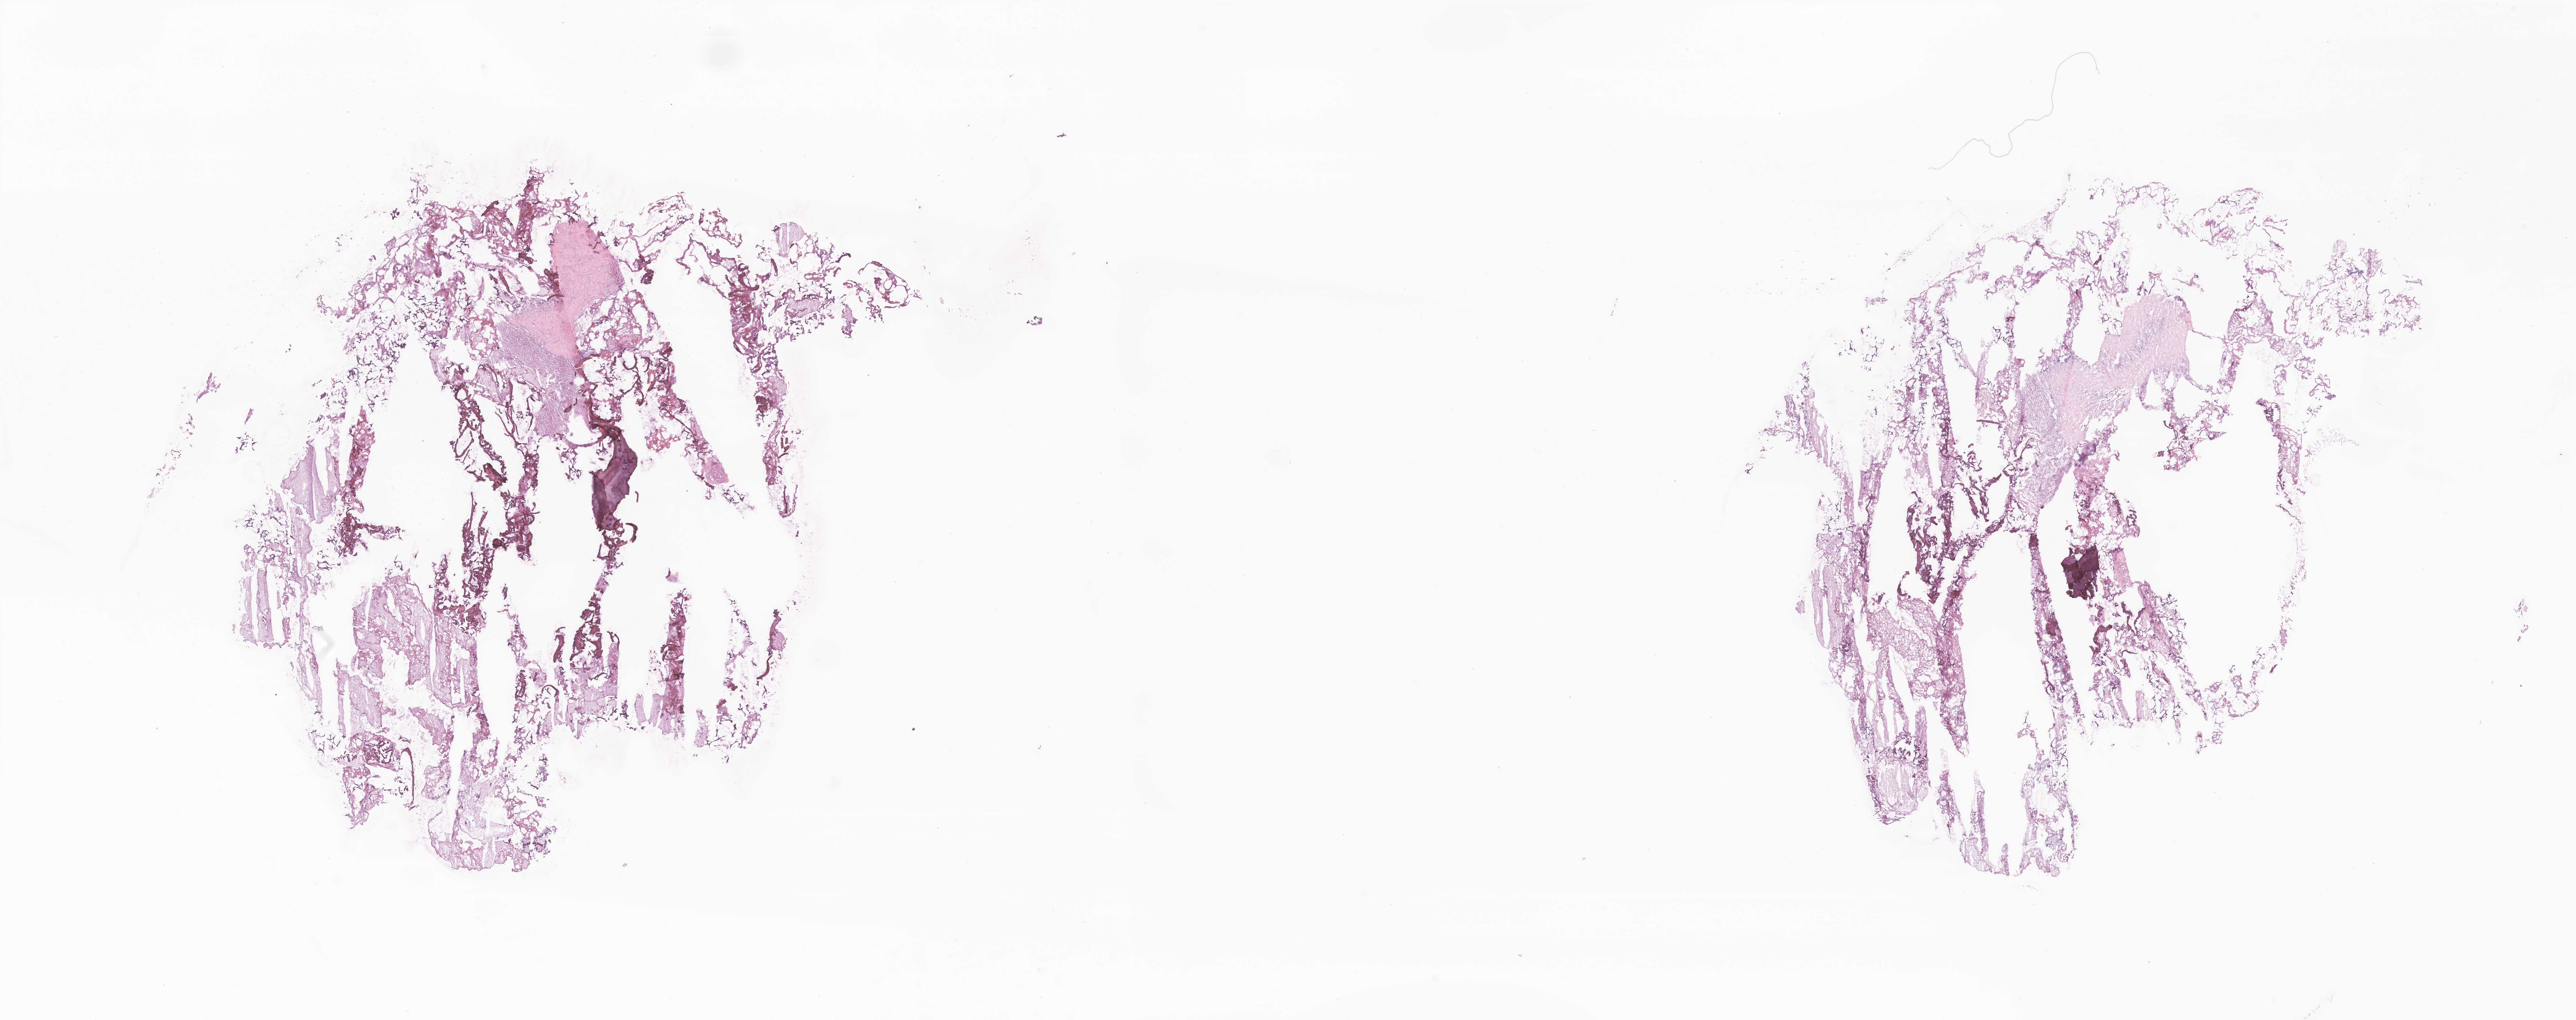
Whole-slide image, hematoxylin and eosin (H&E) stain of tumor tissue from the brain — shown as a low-resolution overview of the whole scanned area (about 33.5 x 13.3 mm). Cryosection (OCT / tissue freezing medium). Patient: female, age 118 months (9 years 10 months).
Diagnosis: Ependymoma, NOS.